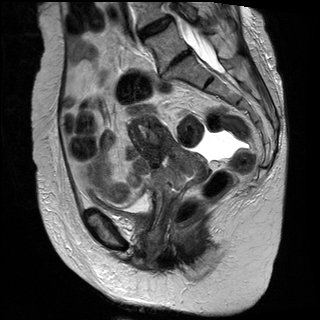
Pelvic MRI for cervical cancer, one sagittal slice. Slice 14 of 30 in the series (ordered by position). T2-weighted. 1.5 T. TE 89 ms, TR 2930 ms. 320 × 320 image matrix. Patient: female, 61 years.
Annotated regions visible in this slice (manually delineated by an expert):
- uterus and cervix: bounding box [x1, y1, x2, y2] px = [129, 115, 208, 206]